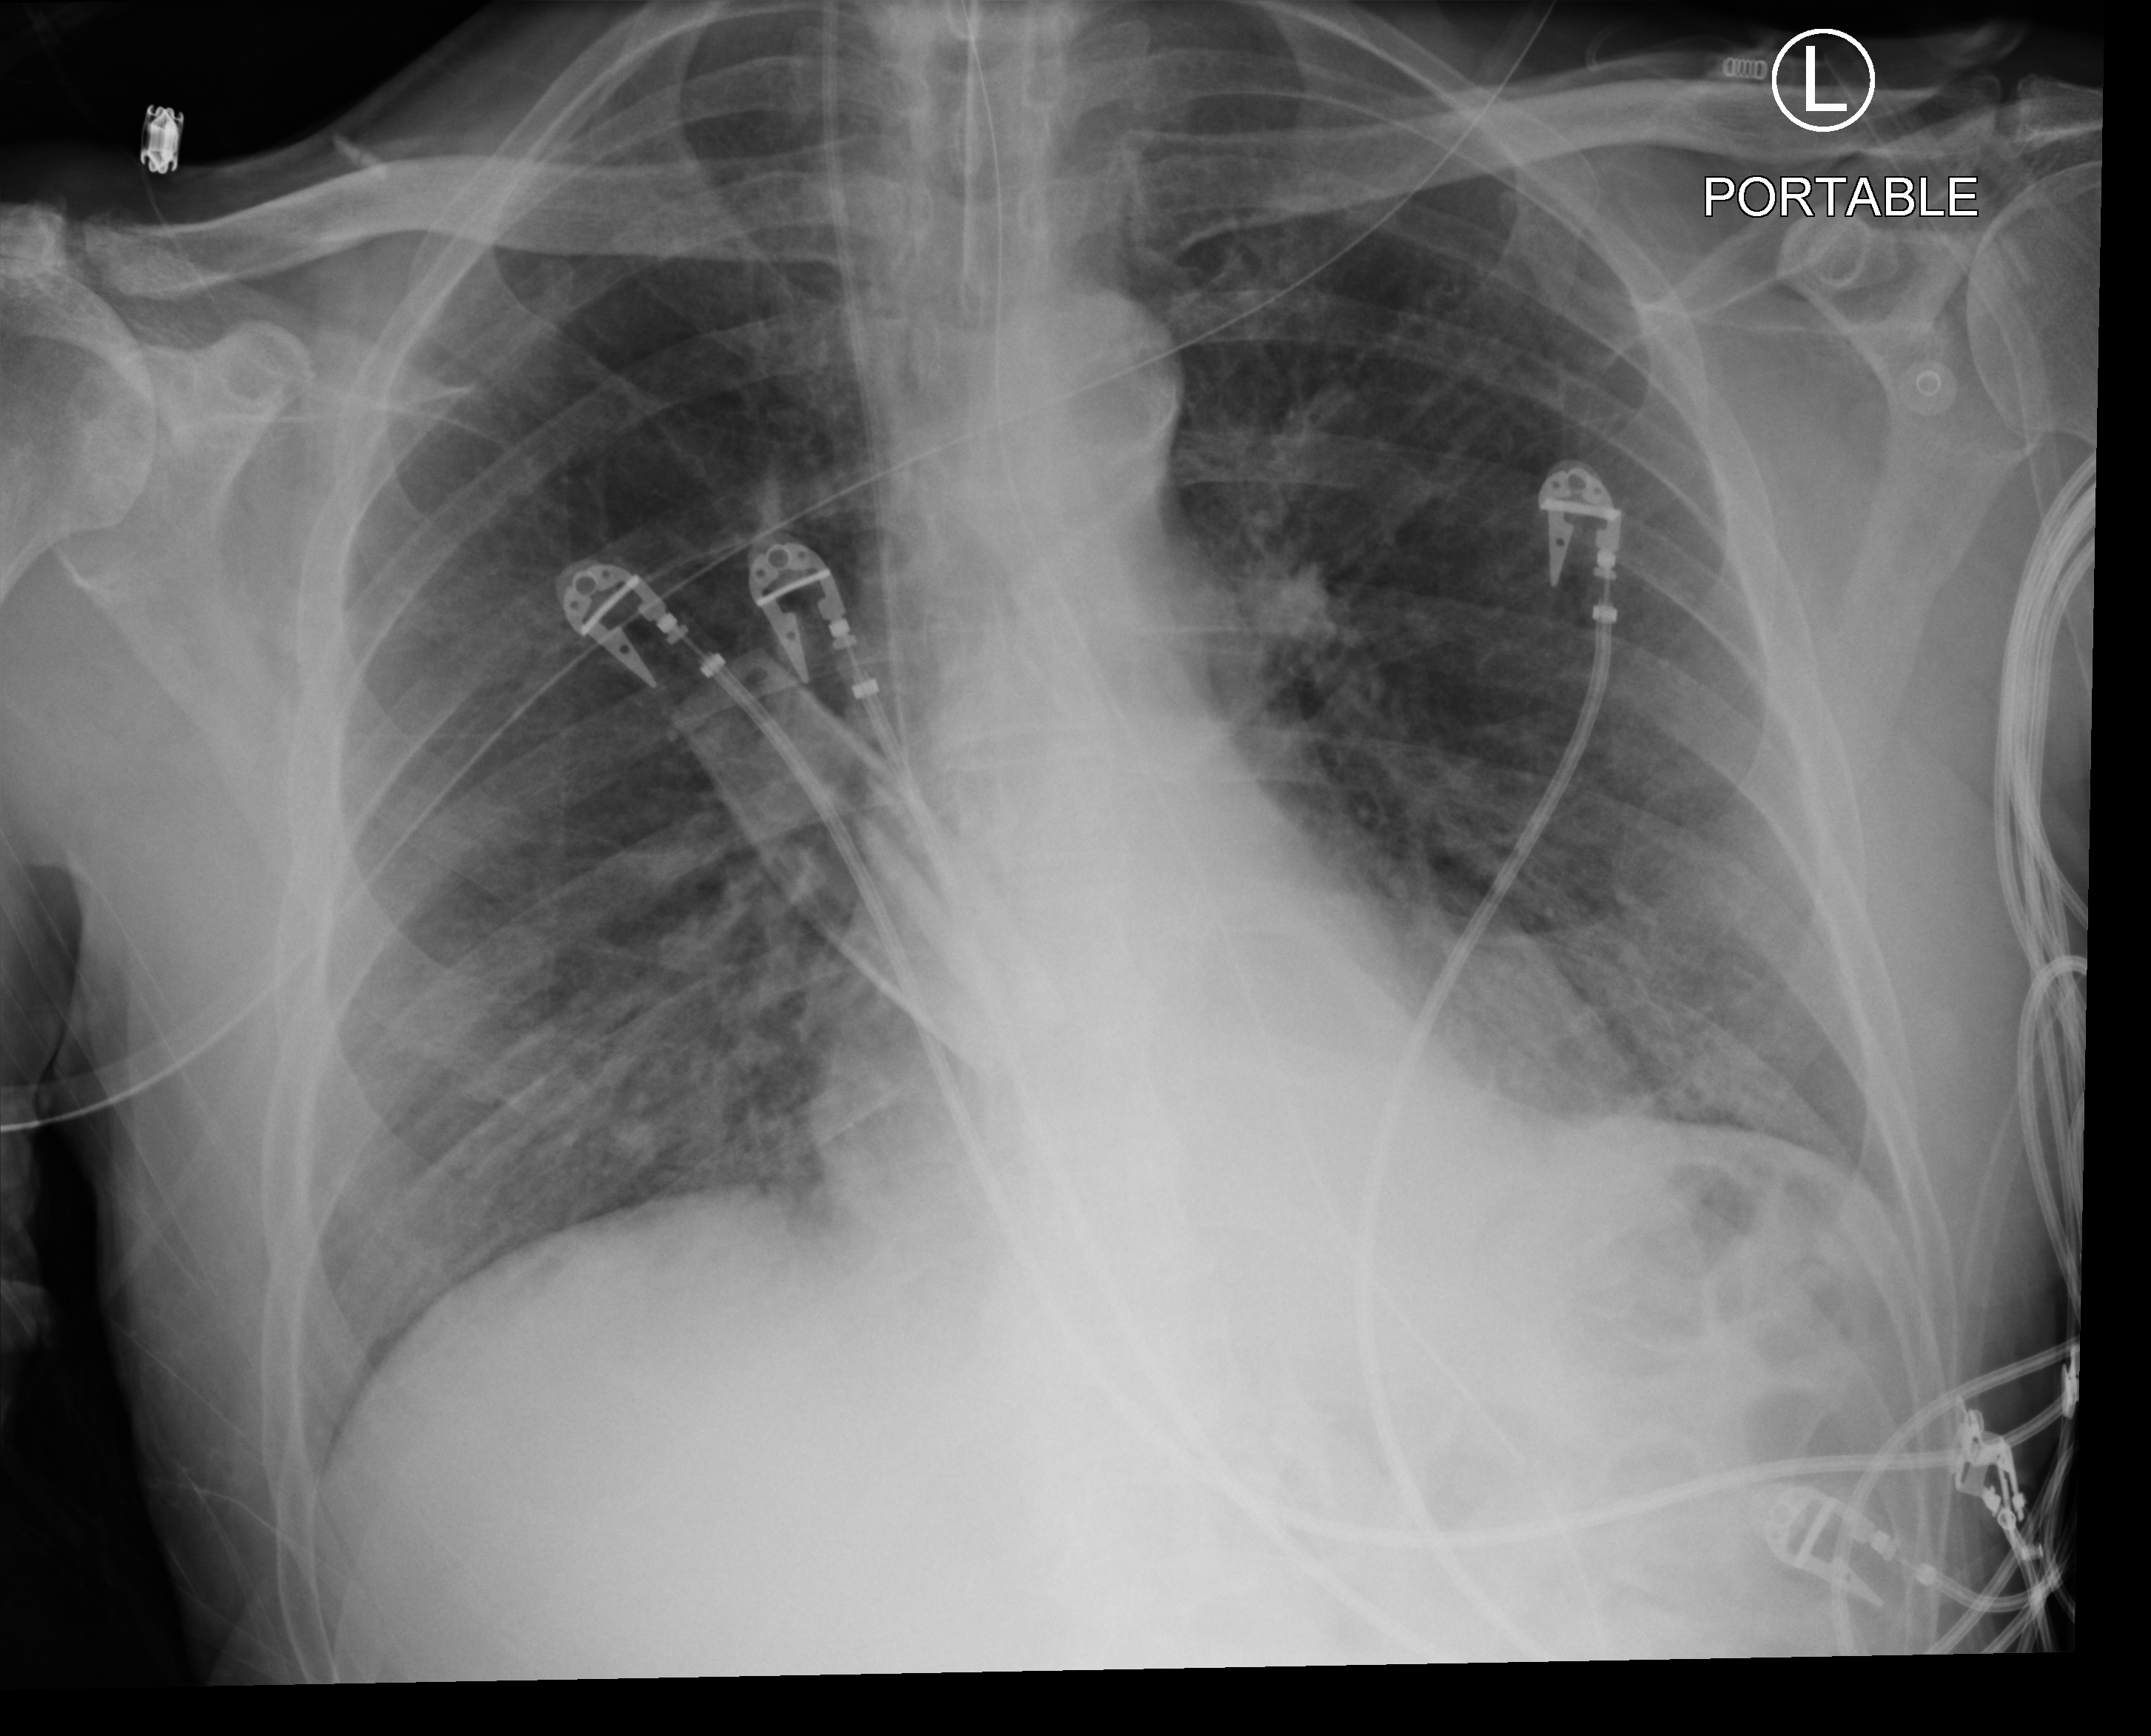
Bedside chest radiograph (computed radiography); anteroposterior (AP) projection. Male patient hospitalised with COVID-19, age 75–90 years.
Hospital-stay facts (about this admission, not read from this image; timing relative to this image not recorded): chronic kidney disease (admission record): no; admitted to intensive care during this hospital stay: yes; mechanically ventilated during this hospital stay: yes.